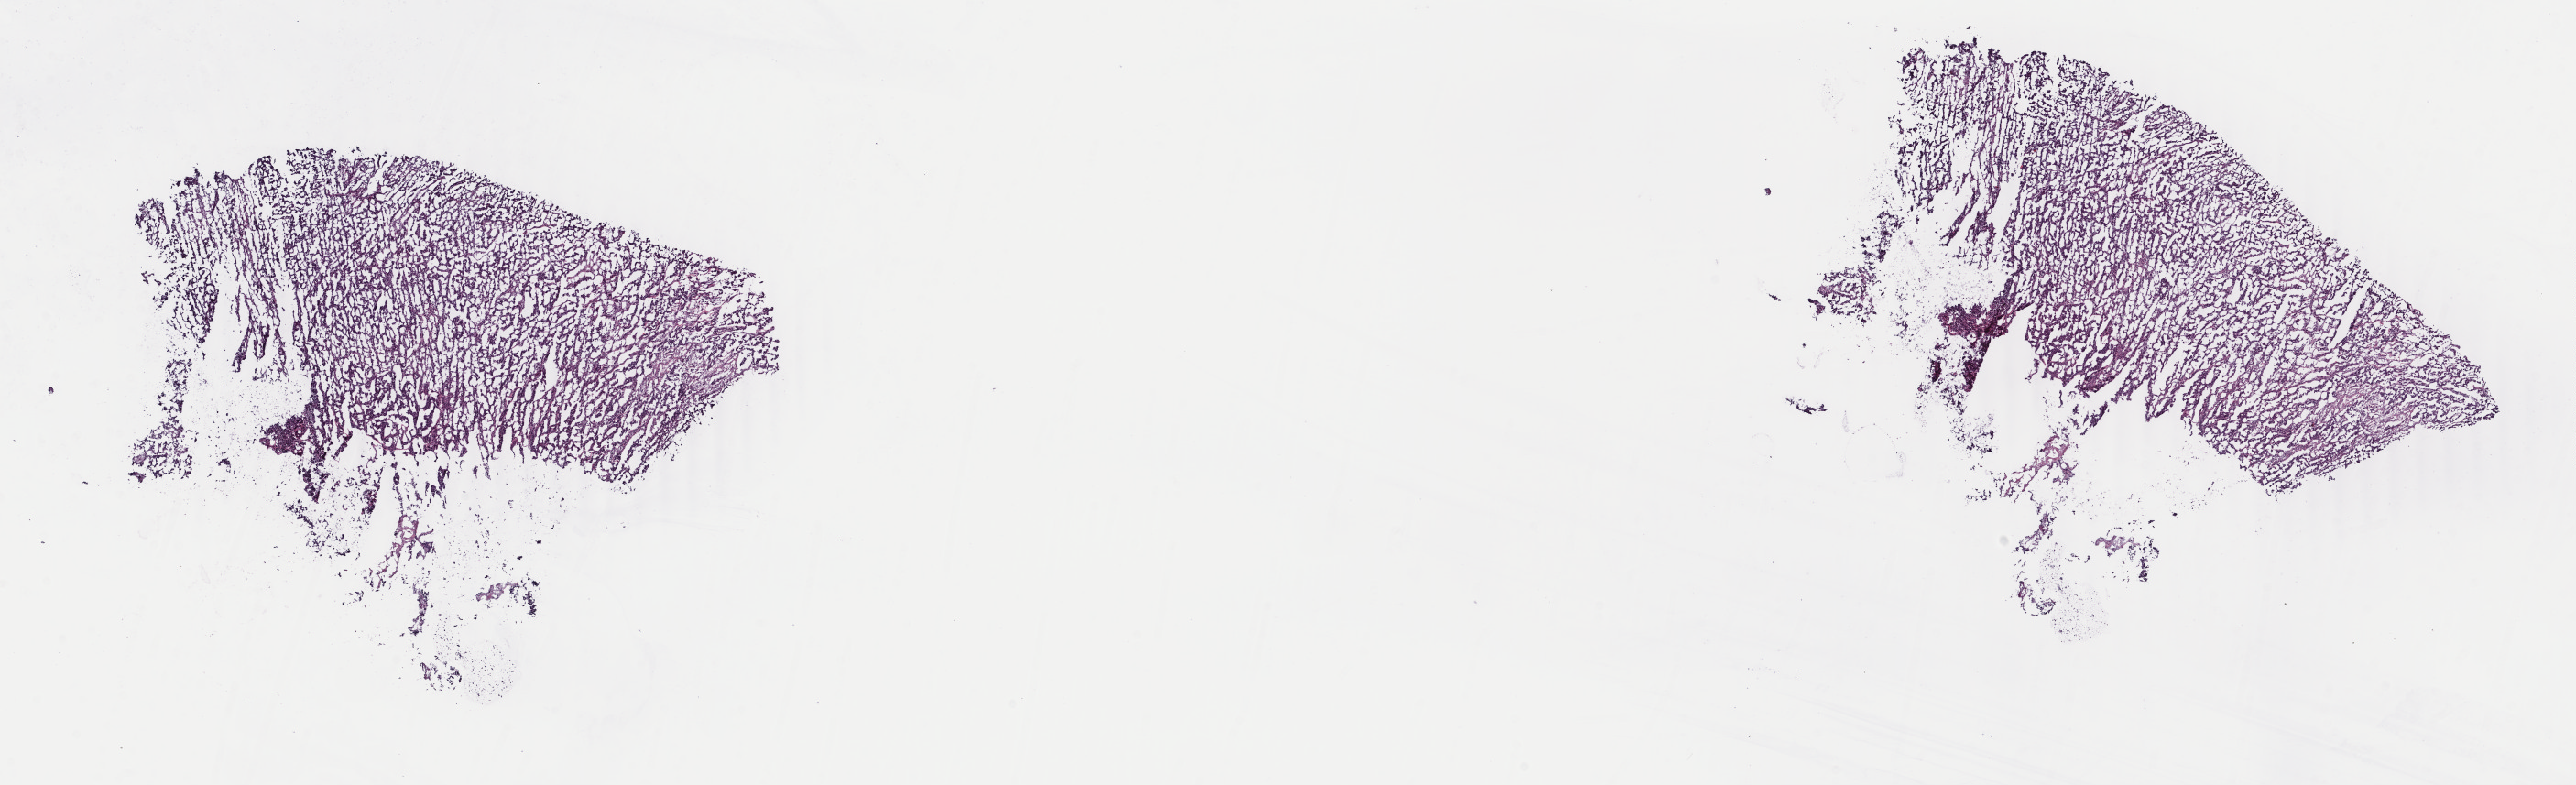
H&E-stained whole-slide image — a low-resolution overview of the entire scanned area, about 22.4 x 6.8 mm (from a 40x scan); frozen section; sample: primary tumour, uterus. Female patient; age at initial diagnosis 65 years. Composition of this section per pathologist review: tumour cells 60%, tumour nuclei 60%, normal cells 30%, stromal cells 5%, necrosis 5%. Infiltration values recorded for this section: lymphocyte infiltration 50%, monocyte infiltration 10%, neutrophil infiltration 20%.
* FIGO stage: IB
* histologic diagnosis: Mullerian mixed tumor
* lymph nodes positive (case pathology): 0 of 12 examined